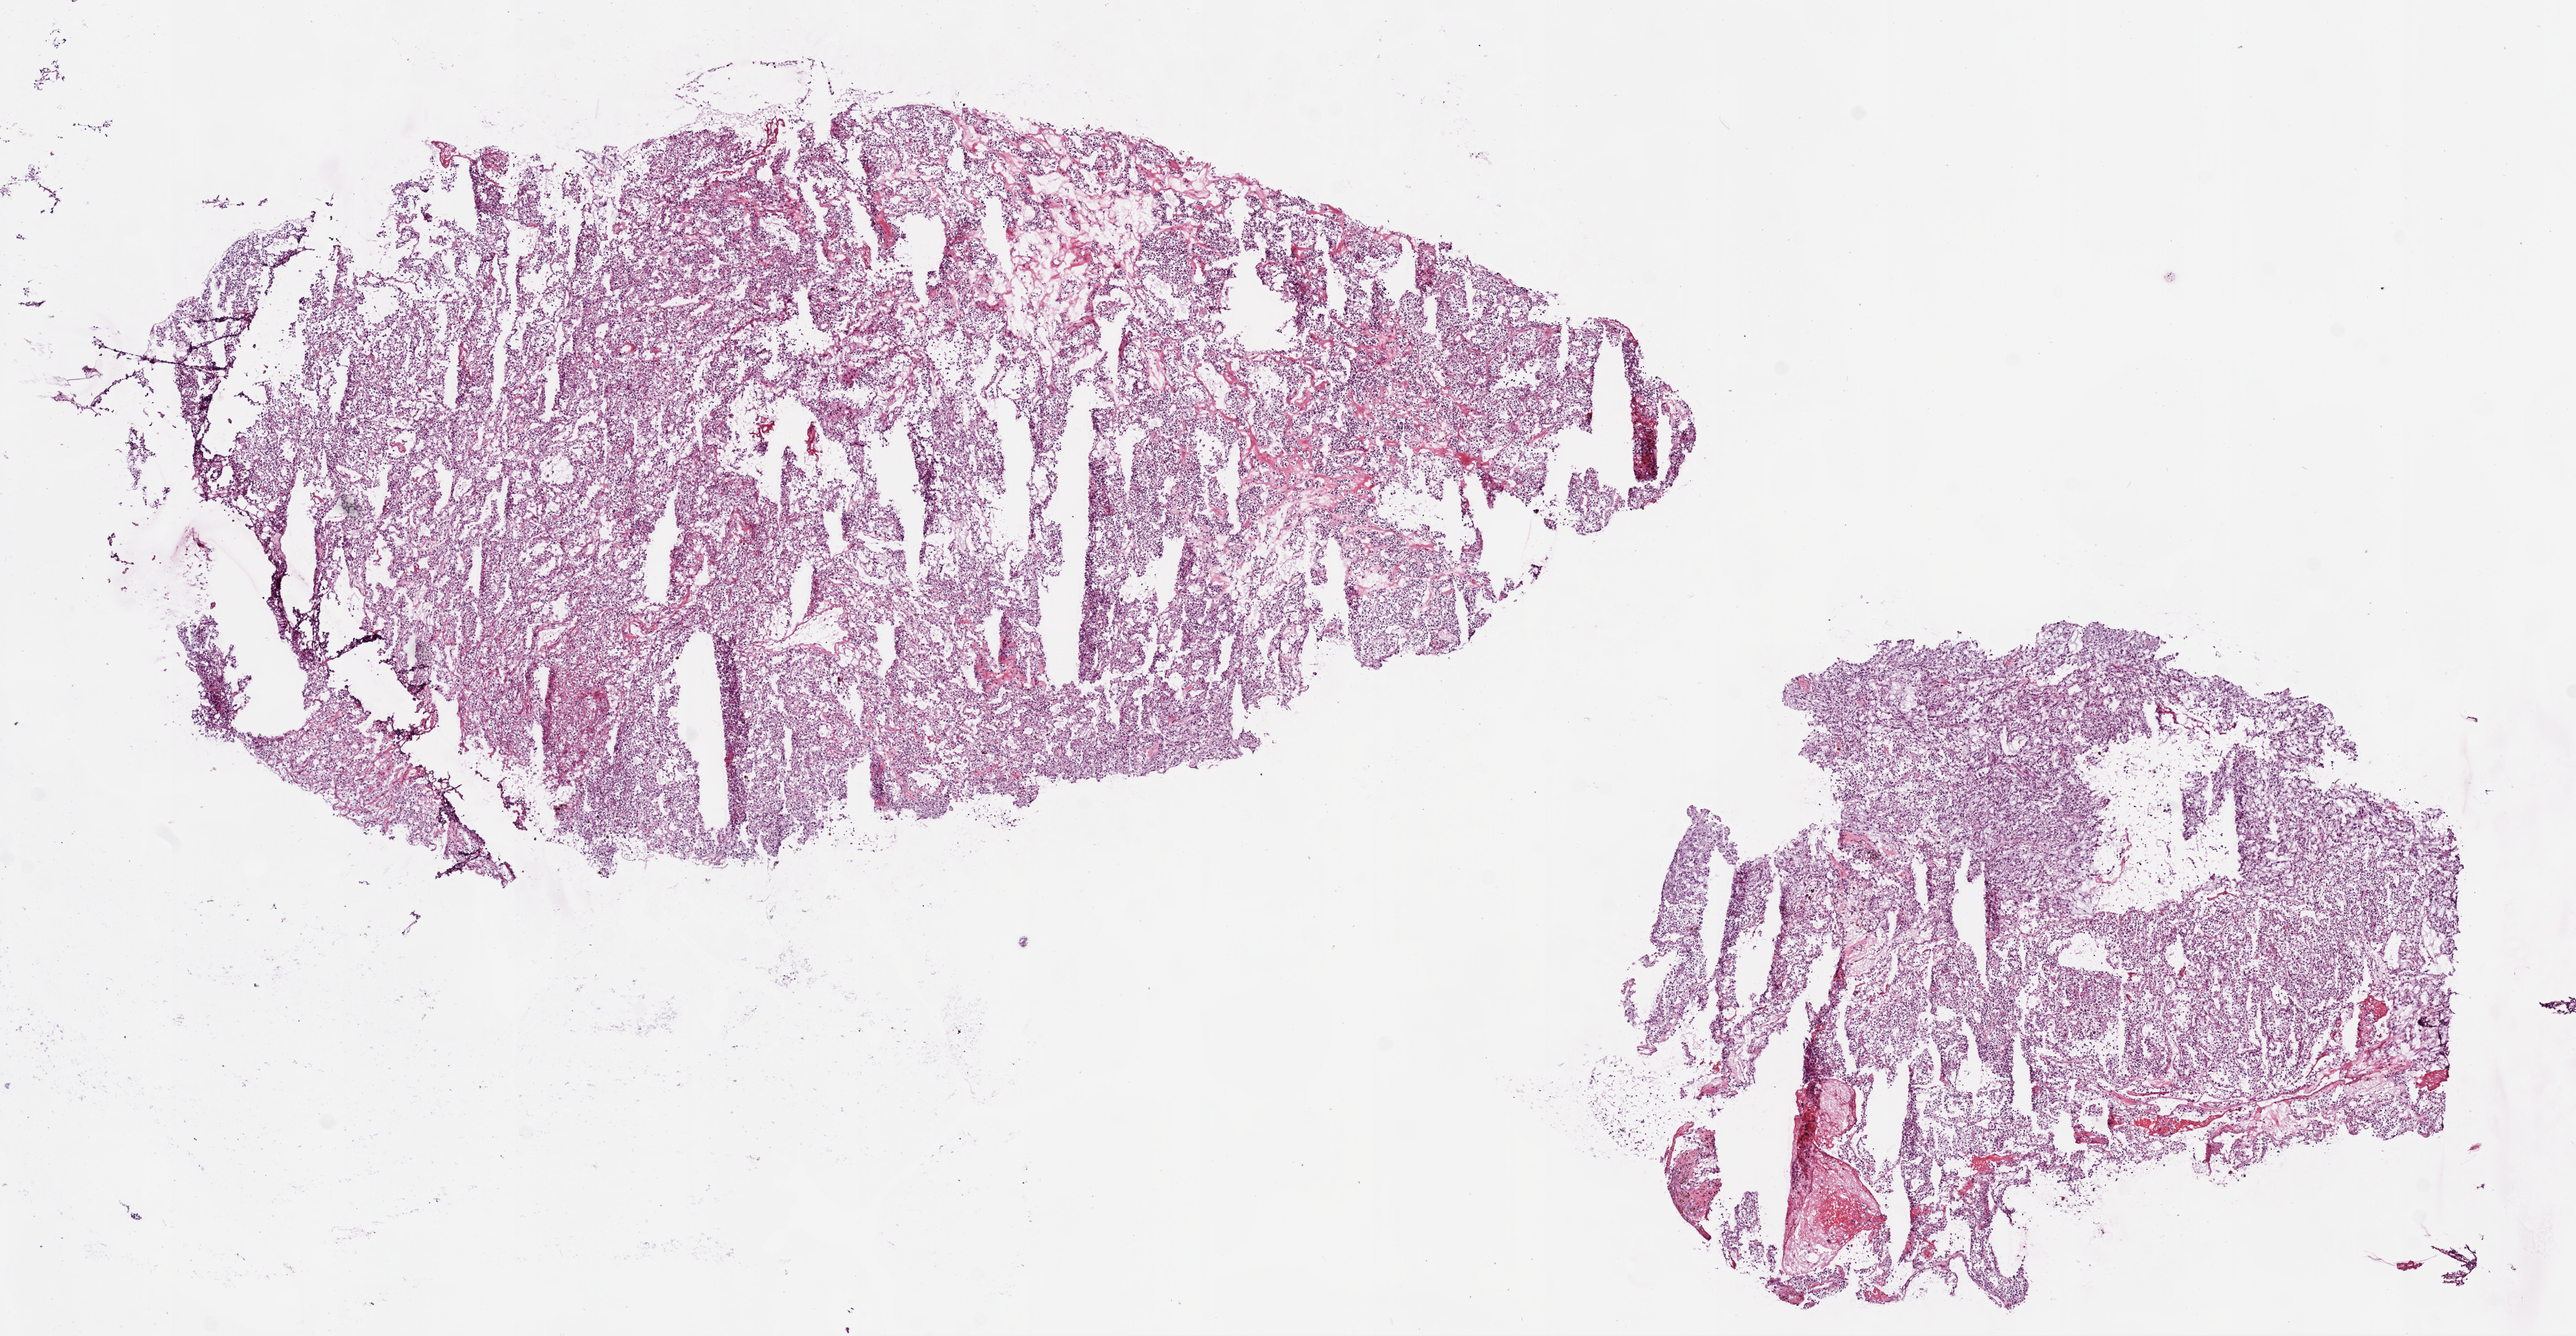
Digitized Hematoxylin and eosin (H&E) stained tissue section (whole slide), low-resolution overview of the scanned area, about 15.0 x 7.8 mm (from a 20x scan). Frozen section from the bottom of the tissue portion. Sample: primary tumour, kidney. Male, age 78 years at initial diagnosis. Histologic grade: G3 (poorly differentiated). Slide review estimates, as recorded: tumour cells 99%, tumour nuclei 95%, stromal cells 1%, necrosis 0%. Infiltration values recorded for this section: lymphocyte infiltration 1%, monocyte infiltration 1%.
• AJCC pathologic stage: I
• diagnosis: Clear cell adenocarcinoma, NOS
• laterality: right